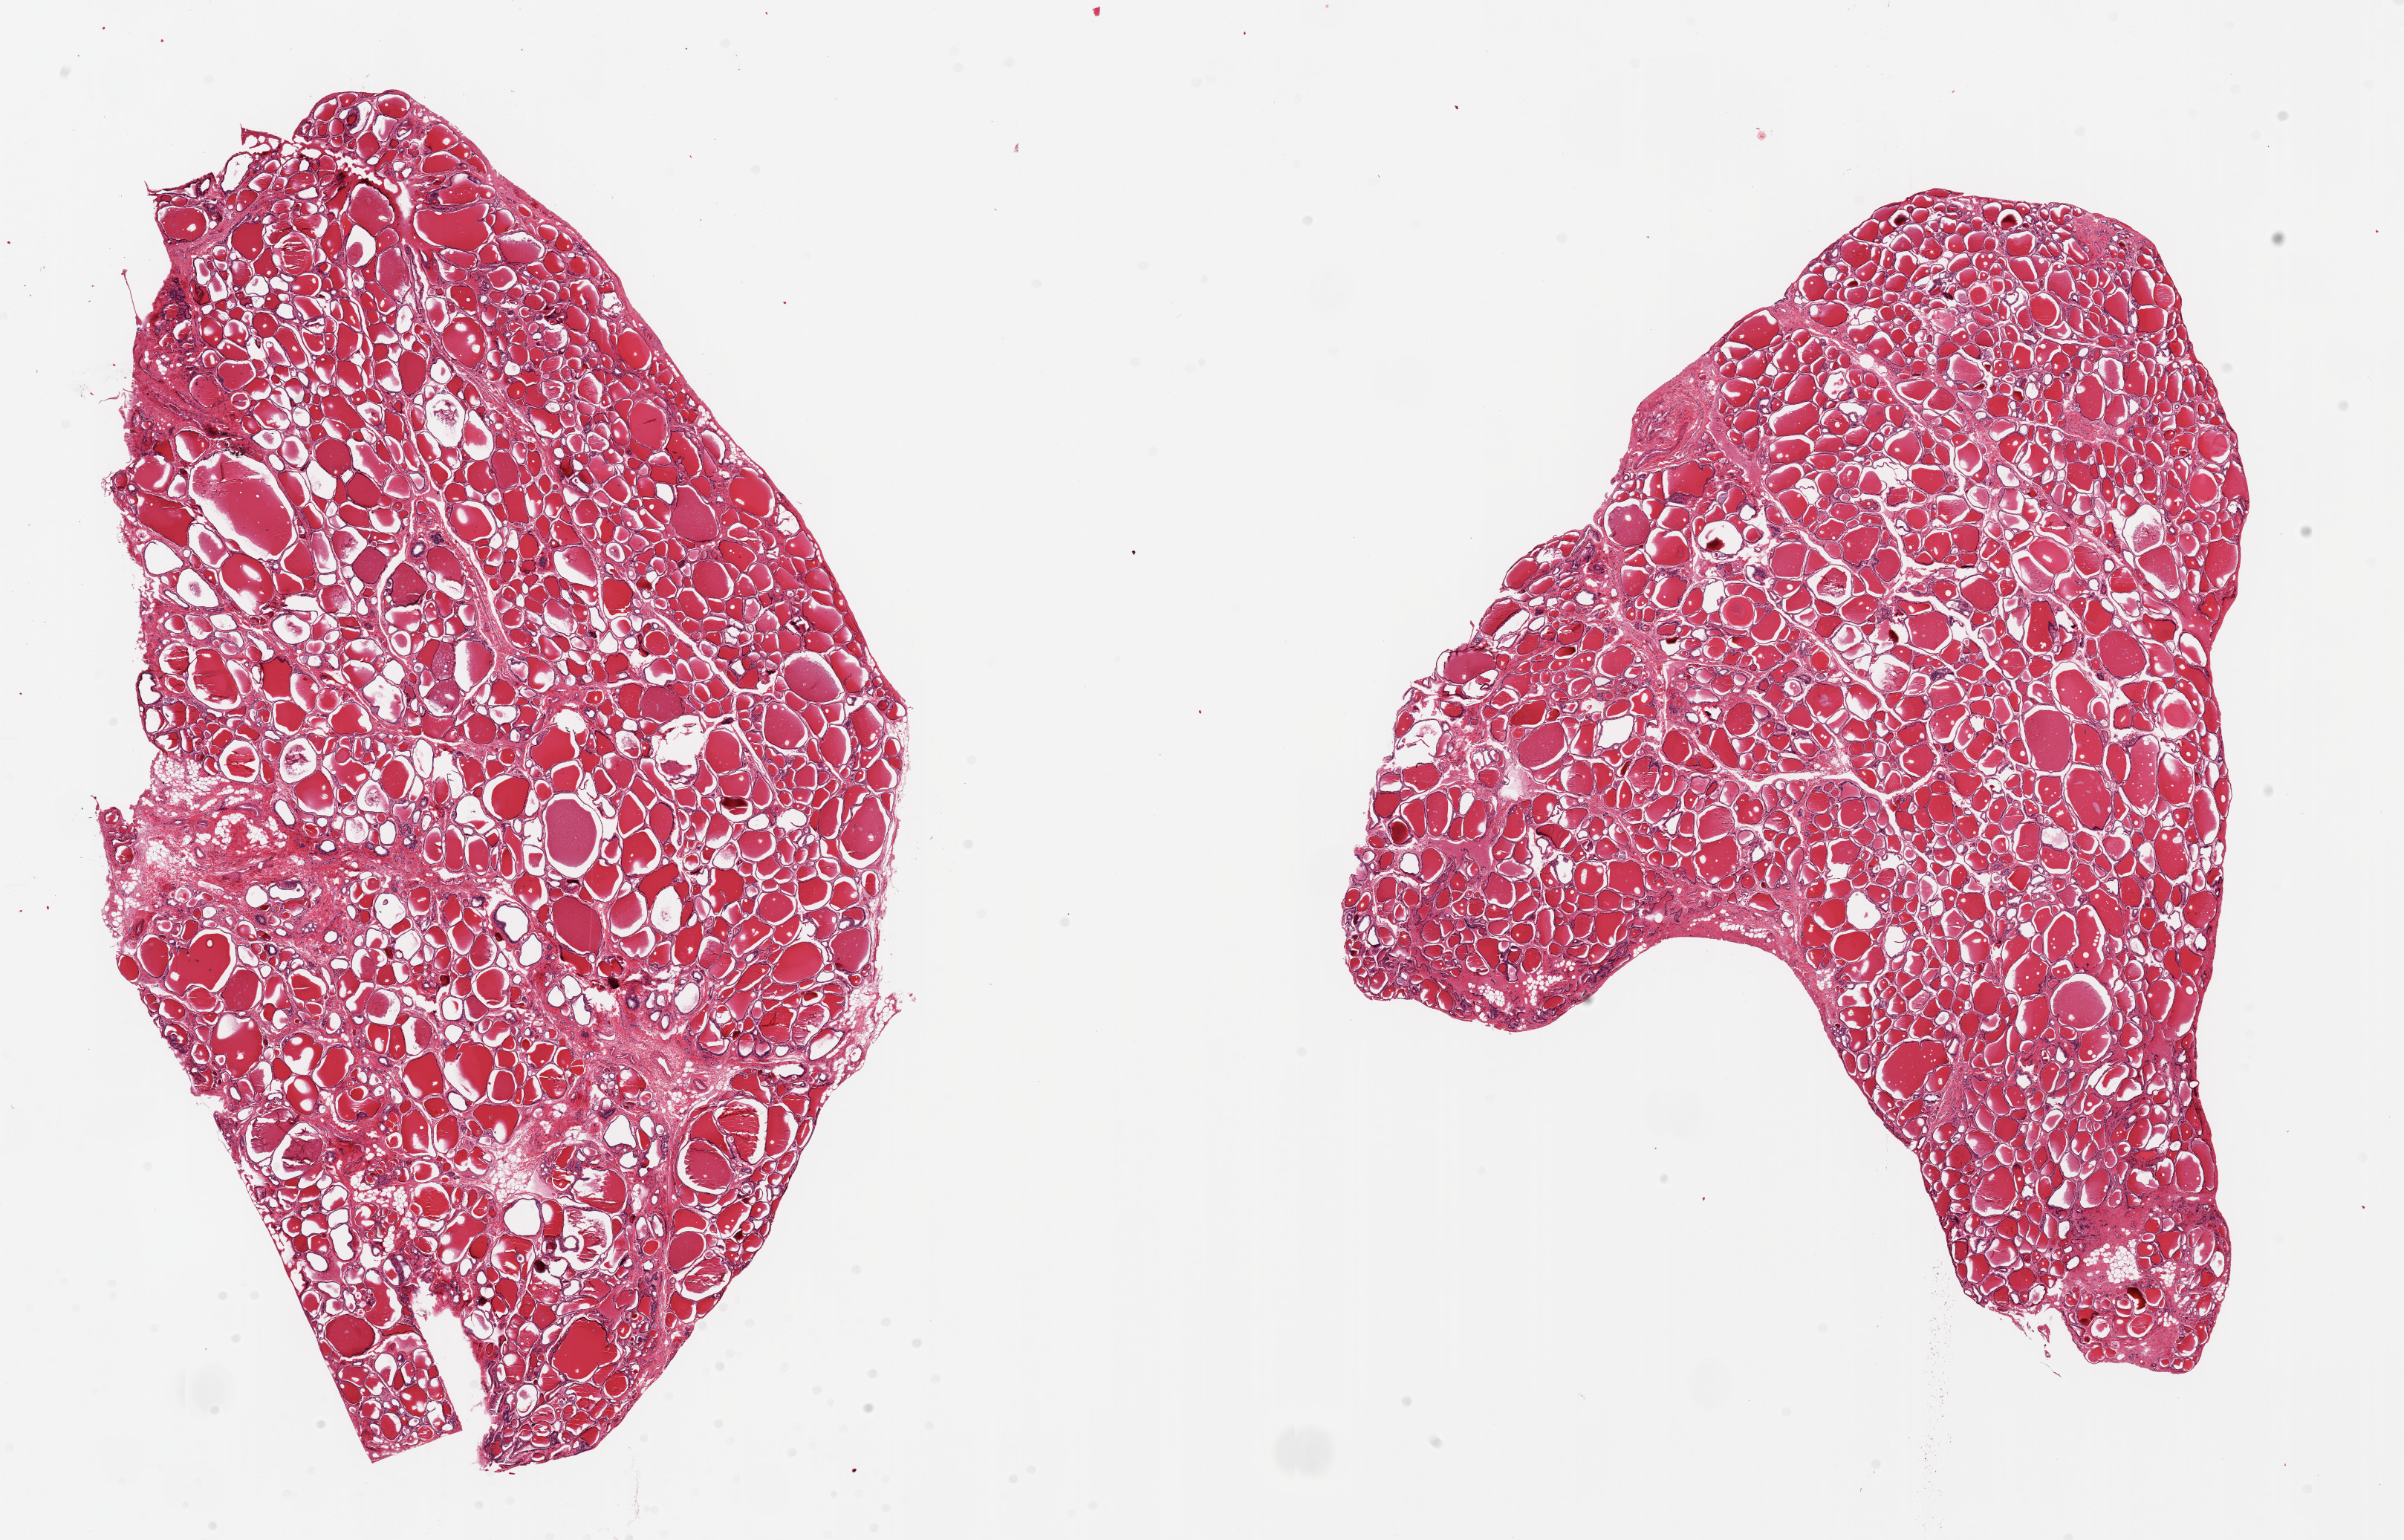
H&E whole-slide image — a low-resolution overview of the entire scanned area, about 25.6 x 16.4 mm. PAXgene-fixed, paraffin-embedded tissue. Target tissue: thyroid. Donor tissue sample. Male donor.
Pathologist's review note for this sample: 2 pieces, no abnormalities.